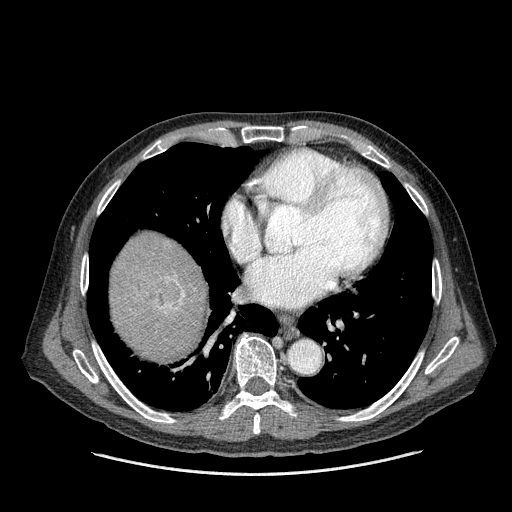
Contrast-enhanced abdominal CT (liver protocol), one axial slice. Slice 154 of 180 in the series (ordered by position). Reconstruction kernel STANDARD. 120 kVp. One of 2 acquisitions stored at this slice position. Soft-tissue window (W 400 / L 40 HU). 2.5 mm slice thickness. 512 × 512 image matrix, field of view 420 × 420 mm. From the clinical record (not read from this slice): diagnosis: hepatocellular carcinoma (patient treated with transarterial chemoembolisation; whether this scan precedes or follows treatment is not stated here); TNM stage (as recorded): Stage-II; Child-Pugh class: A; tumour nodularity: multinodular; tumour size: 2.8 cm.
Outlined on this slice (semi-automatically segmented with operator editing):
- liver parenchyma outside the tumour (the mass and vessels are separate outlines, so this box may not span the whole liver): bounding box <110,232,206,358> (left, top, right, bottom; pixels)
- mass: <140,271,185,312>